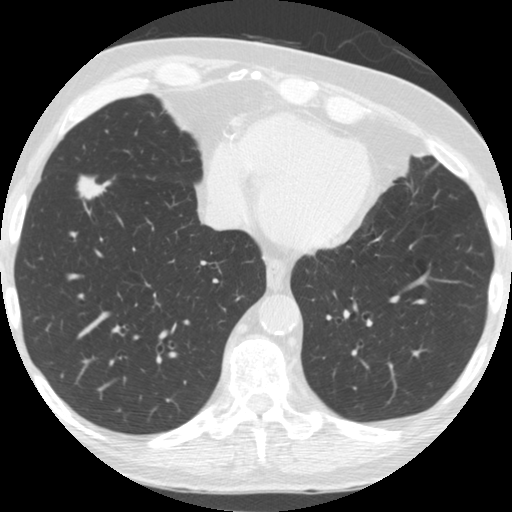
Low-dose screening chest CT, one axial slice. Slice 67 of 182 in the series (ordered by position). Reconstruction kernel STANDARD. 120 kVp. Lung window (W 1500 / L -600 HU). 2.5 mm slice thickness. 512 × 512 image matrix, field of view 320 × 320 mm.
Outlined on this slice (outlined manually by an expert reader):
- lesion 1 (tumor, lower lobe of right lung): bounding box [x1, y1, x2, y2] px = [77, 175, 109, 205]